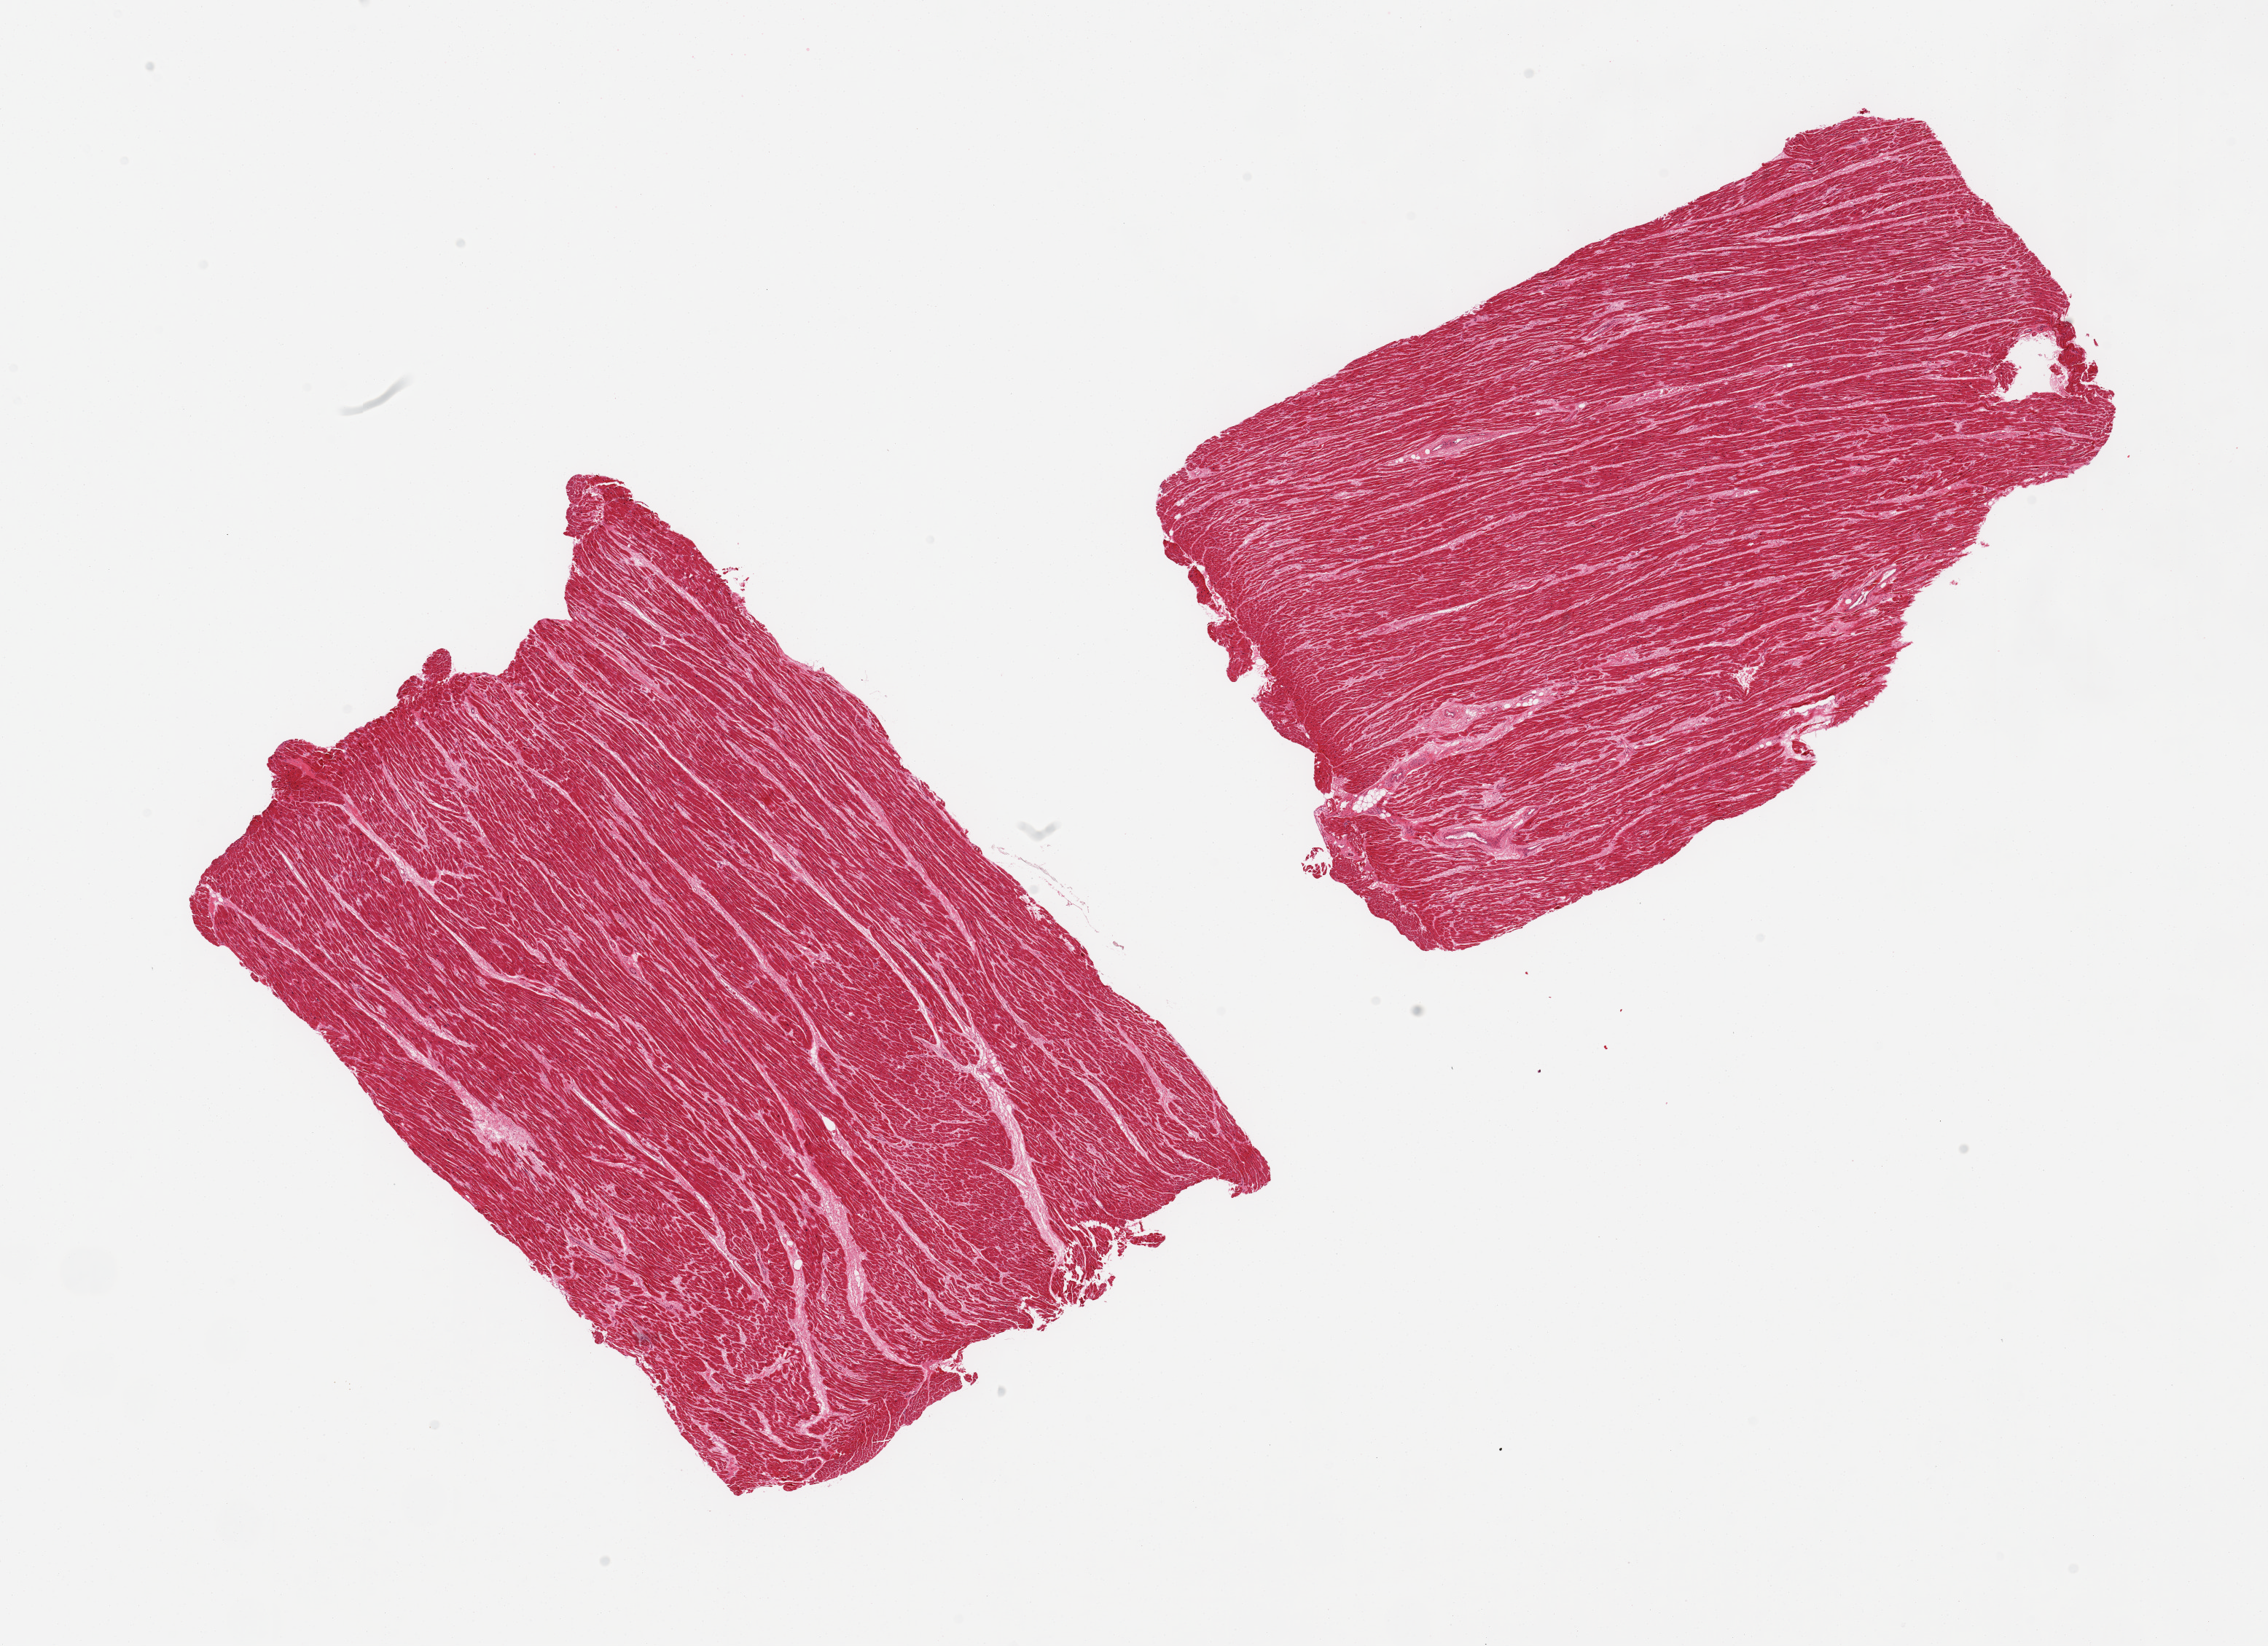
Whole-slide image, haematoxylin and eosin stain, whole scanned area (about 24.6 x 17.9 mm, slide scanned at 20x) shown as a low-resolution overview; PAXgene-fixed, paraffin-embedded tissue; section of heart (target tissue); tissue donor sample. Donor sex: male.
* review note (as recorded): 2 pieces; minimal fat